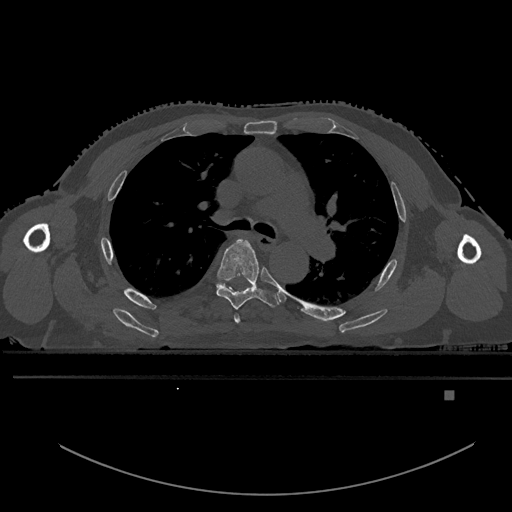
CT including the spine, one axial slice. Position 359 of 969 along the scan axis. Bone window (W 1800 / L 400 HU). 0.5 mm slice thickness. 512 × 512 image matrix, field of view 456 × 456 mm. Patient: male, 82 years. From the clinical record (not read from this slice): primary cancer: prostate; vertebrae with lytic lesions (as recorded): T11, T9, T8, T2.
Structures marked on this image (semi-automatic segmentation, software-assisted and operator-edited):
- T4 vertebra: bounding box (x1, y1, x2, y2) in pixels: (234, 314, 241, 324)
- T5 vertebra: (216, 239, 279, 310)